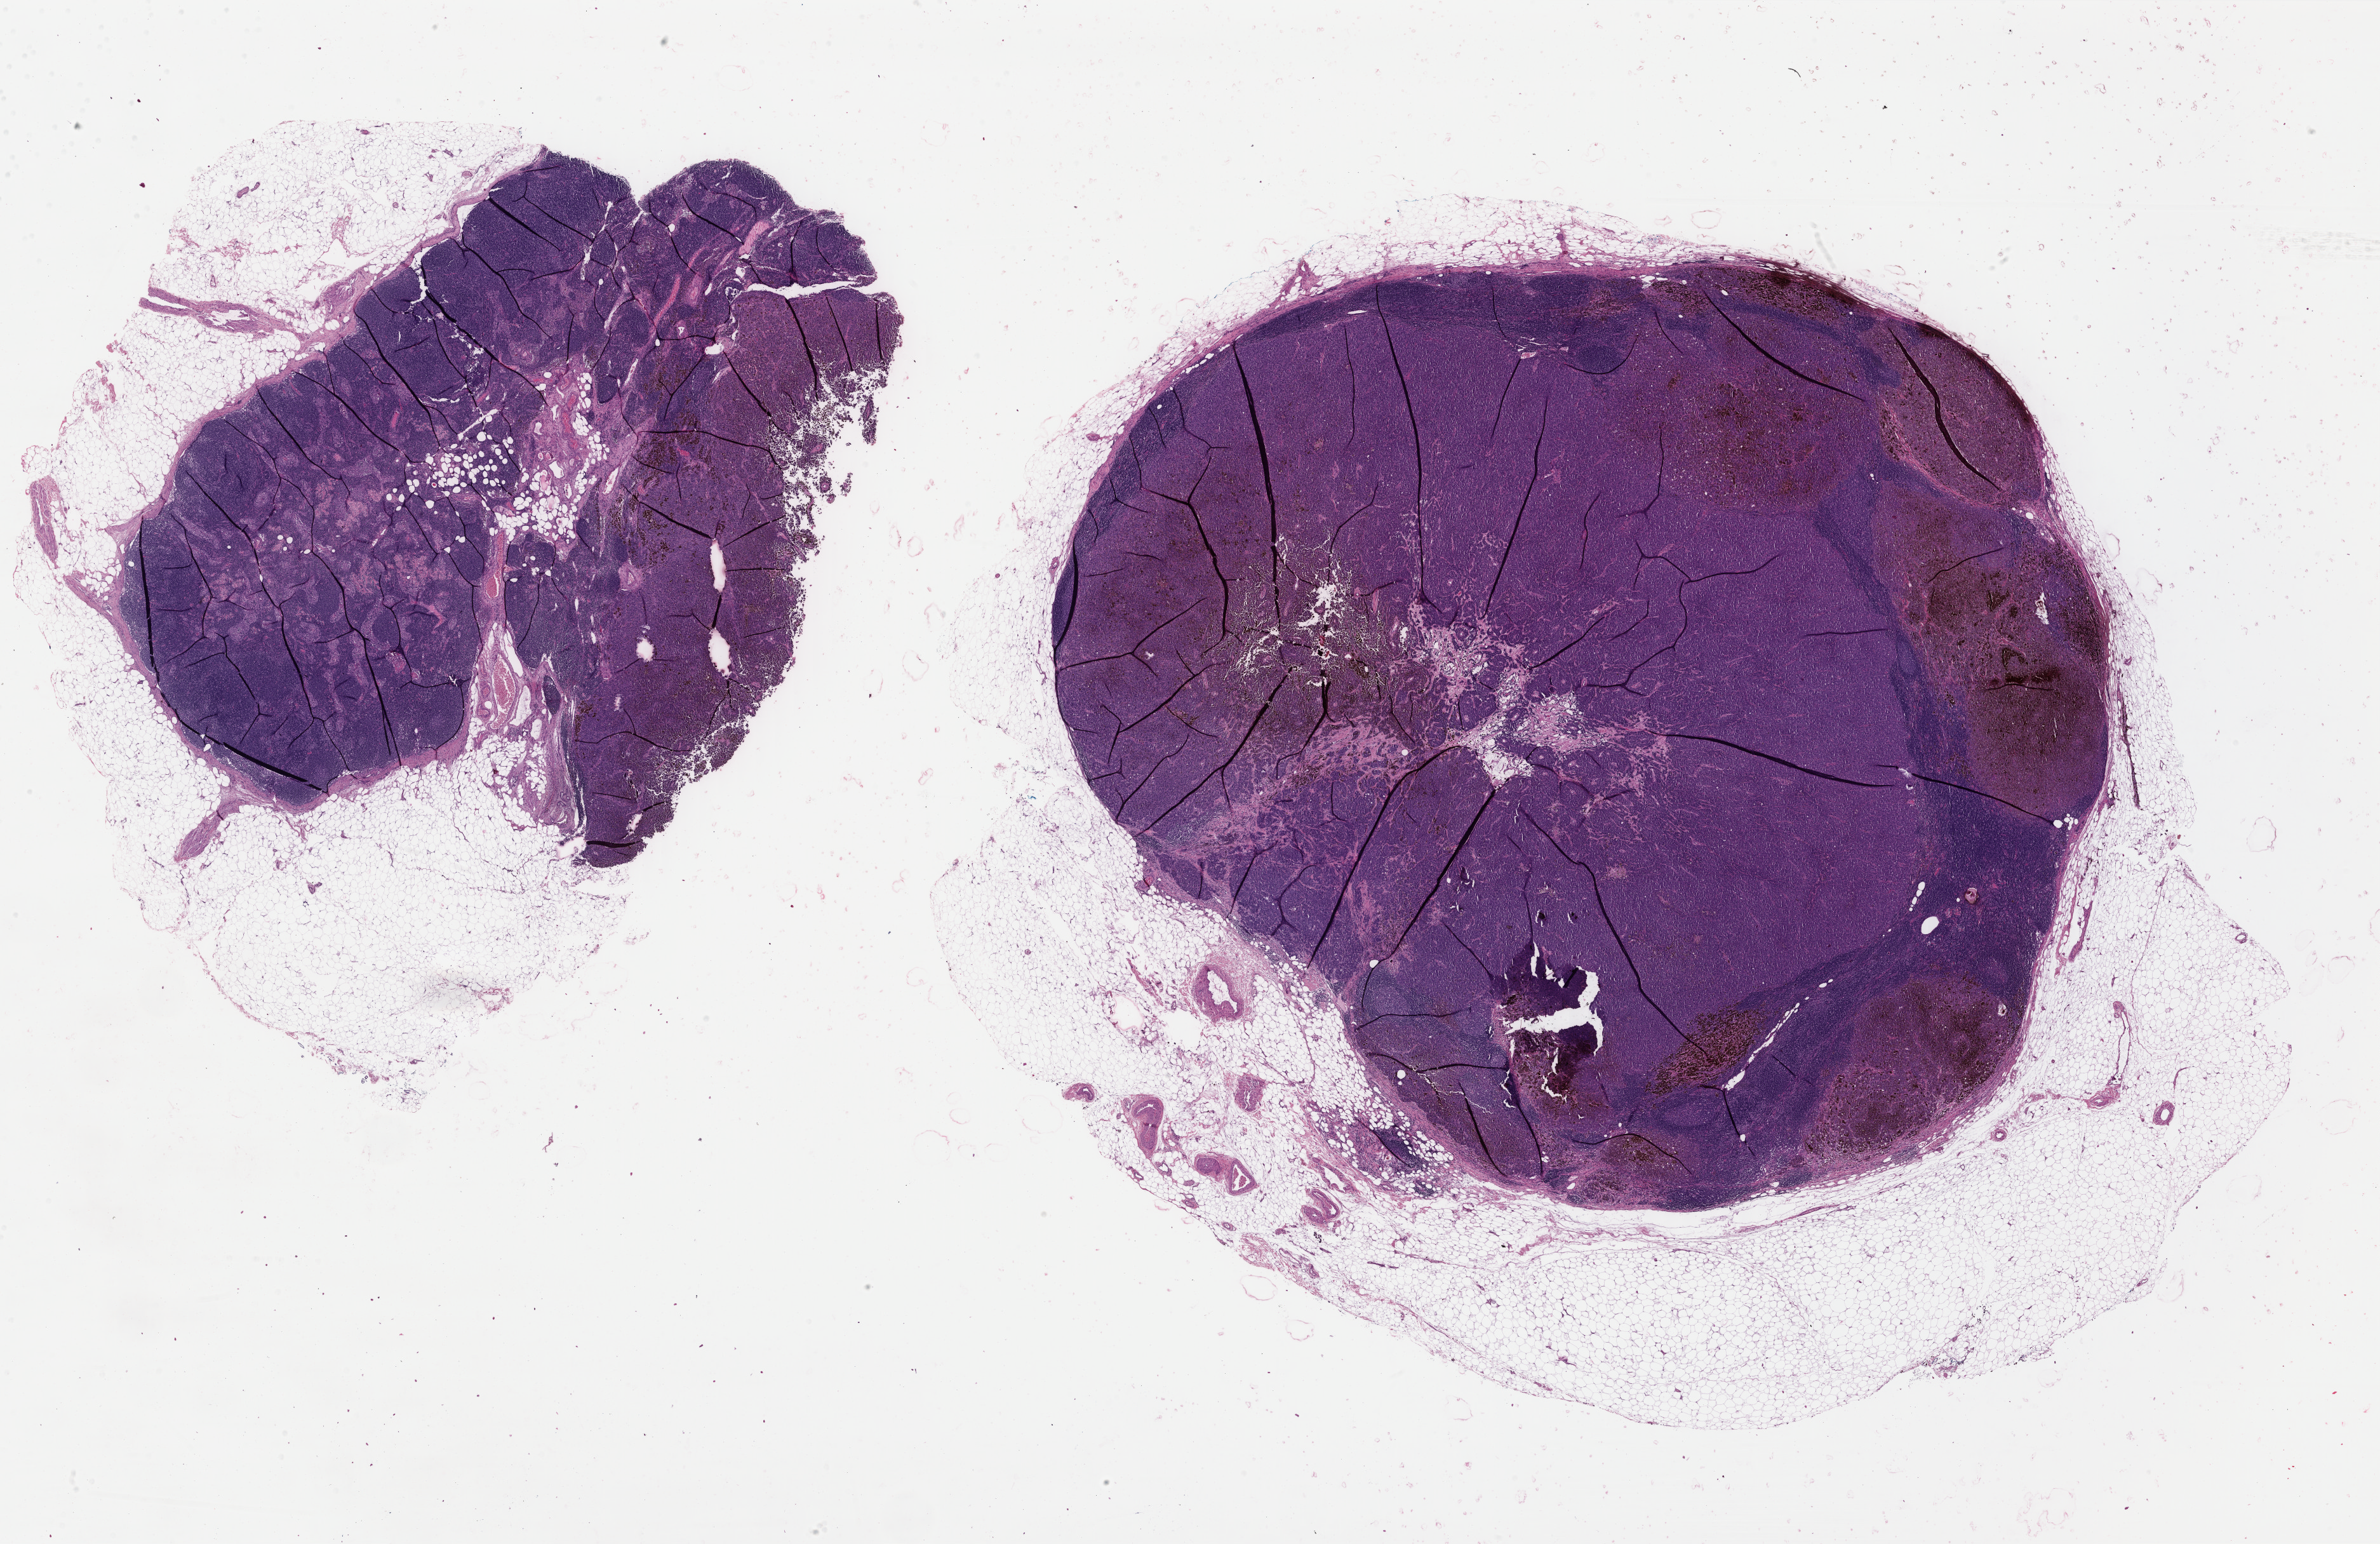
Whole-slide histology image, Hematoxylin and eosin (H&E) stained — shown as a low-resolution overview of the whole scanned area (about 29.7 x 19.3 mm, acquisition: 40x scan). Formalin-fixed paraffin-embedded (FFPE) diagnostic section. Sample: primary tumour, skin. Patient: male, age at initial diagnosis 77 years.
Diagnosis: Malignant melanoma, NOS.